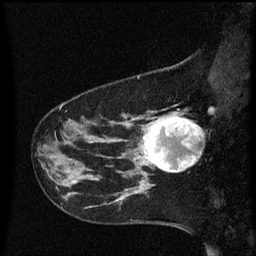
Breast MRI (dynamic contrast-enhanced), one sagittal slice; slice 17 of 60 in the series (ordered by position); dynamic contrast-enhanced series, image 2 of 3 at this slice position (ordered by acquisition); 1.5 T; TE 4.2 ms, TR 8.4 ms; 256 × 256 image matrix. Female patient, age 41 years. From the clinical record (not read from this slice): setting: breast cancer imaged before/during neoadjuvant chemotherapy; receptor status: triple-negative.
Structures marked on this image (semi-automatic segmentation, software-assisted and operator-edited):
- analysis volume of interest (the breast-tissue region the enhancement analysis was run in; not a lesion): box from (x=138, y=112) to (x=202, y=177) px
- tumour enhancement mask (voxels above the 70 % enhancement threshold inside the analysis volume of interest): (x=143, y=116)–(x=199, y=173)